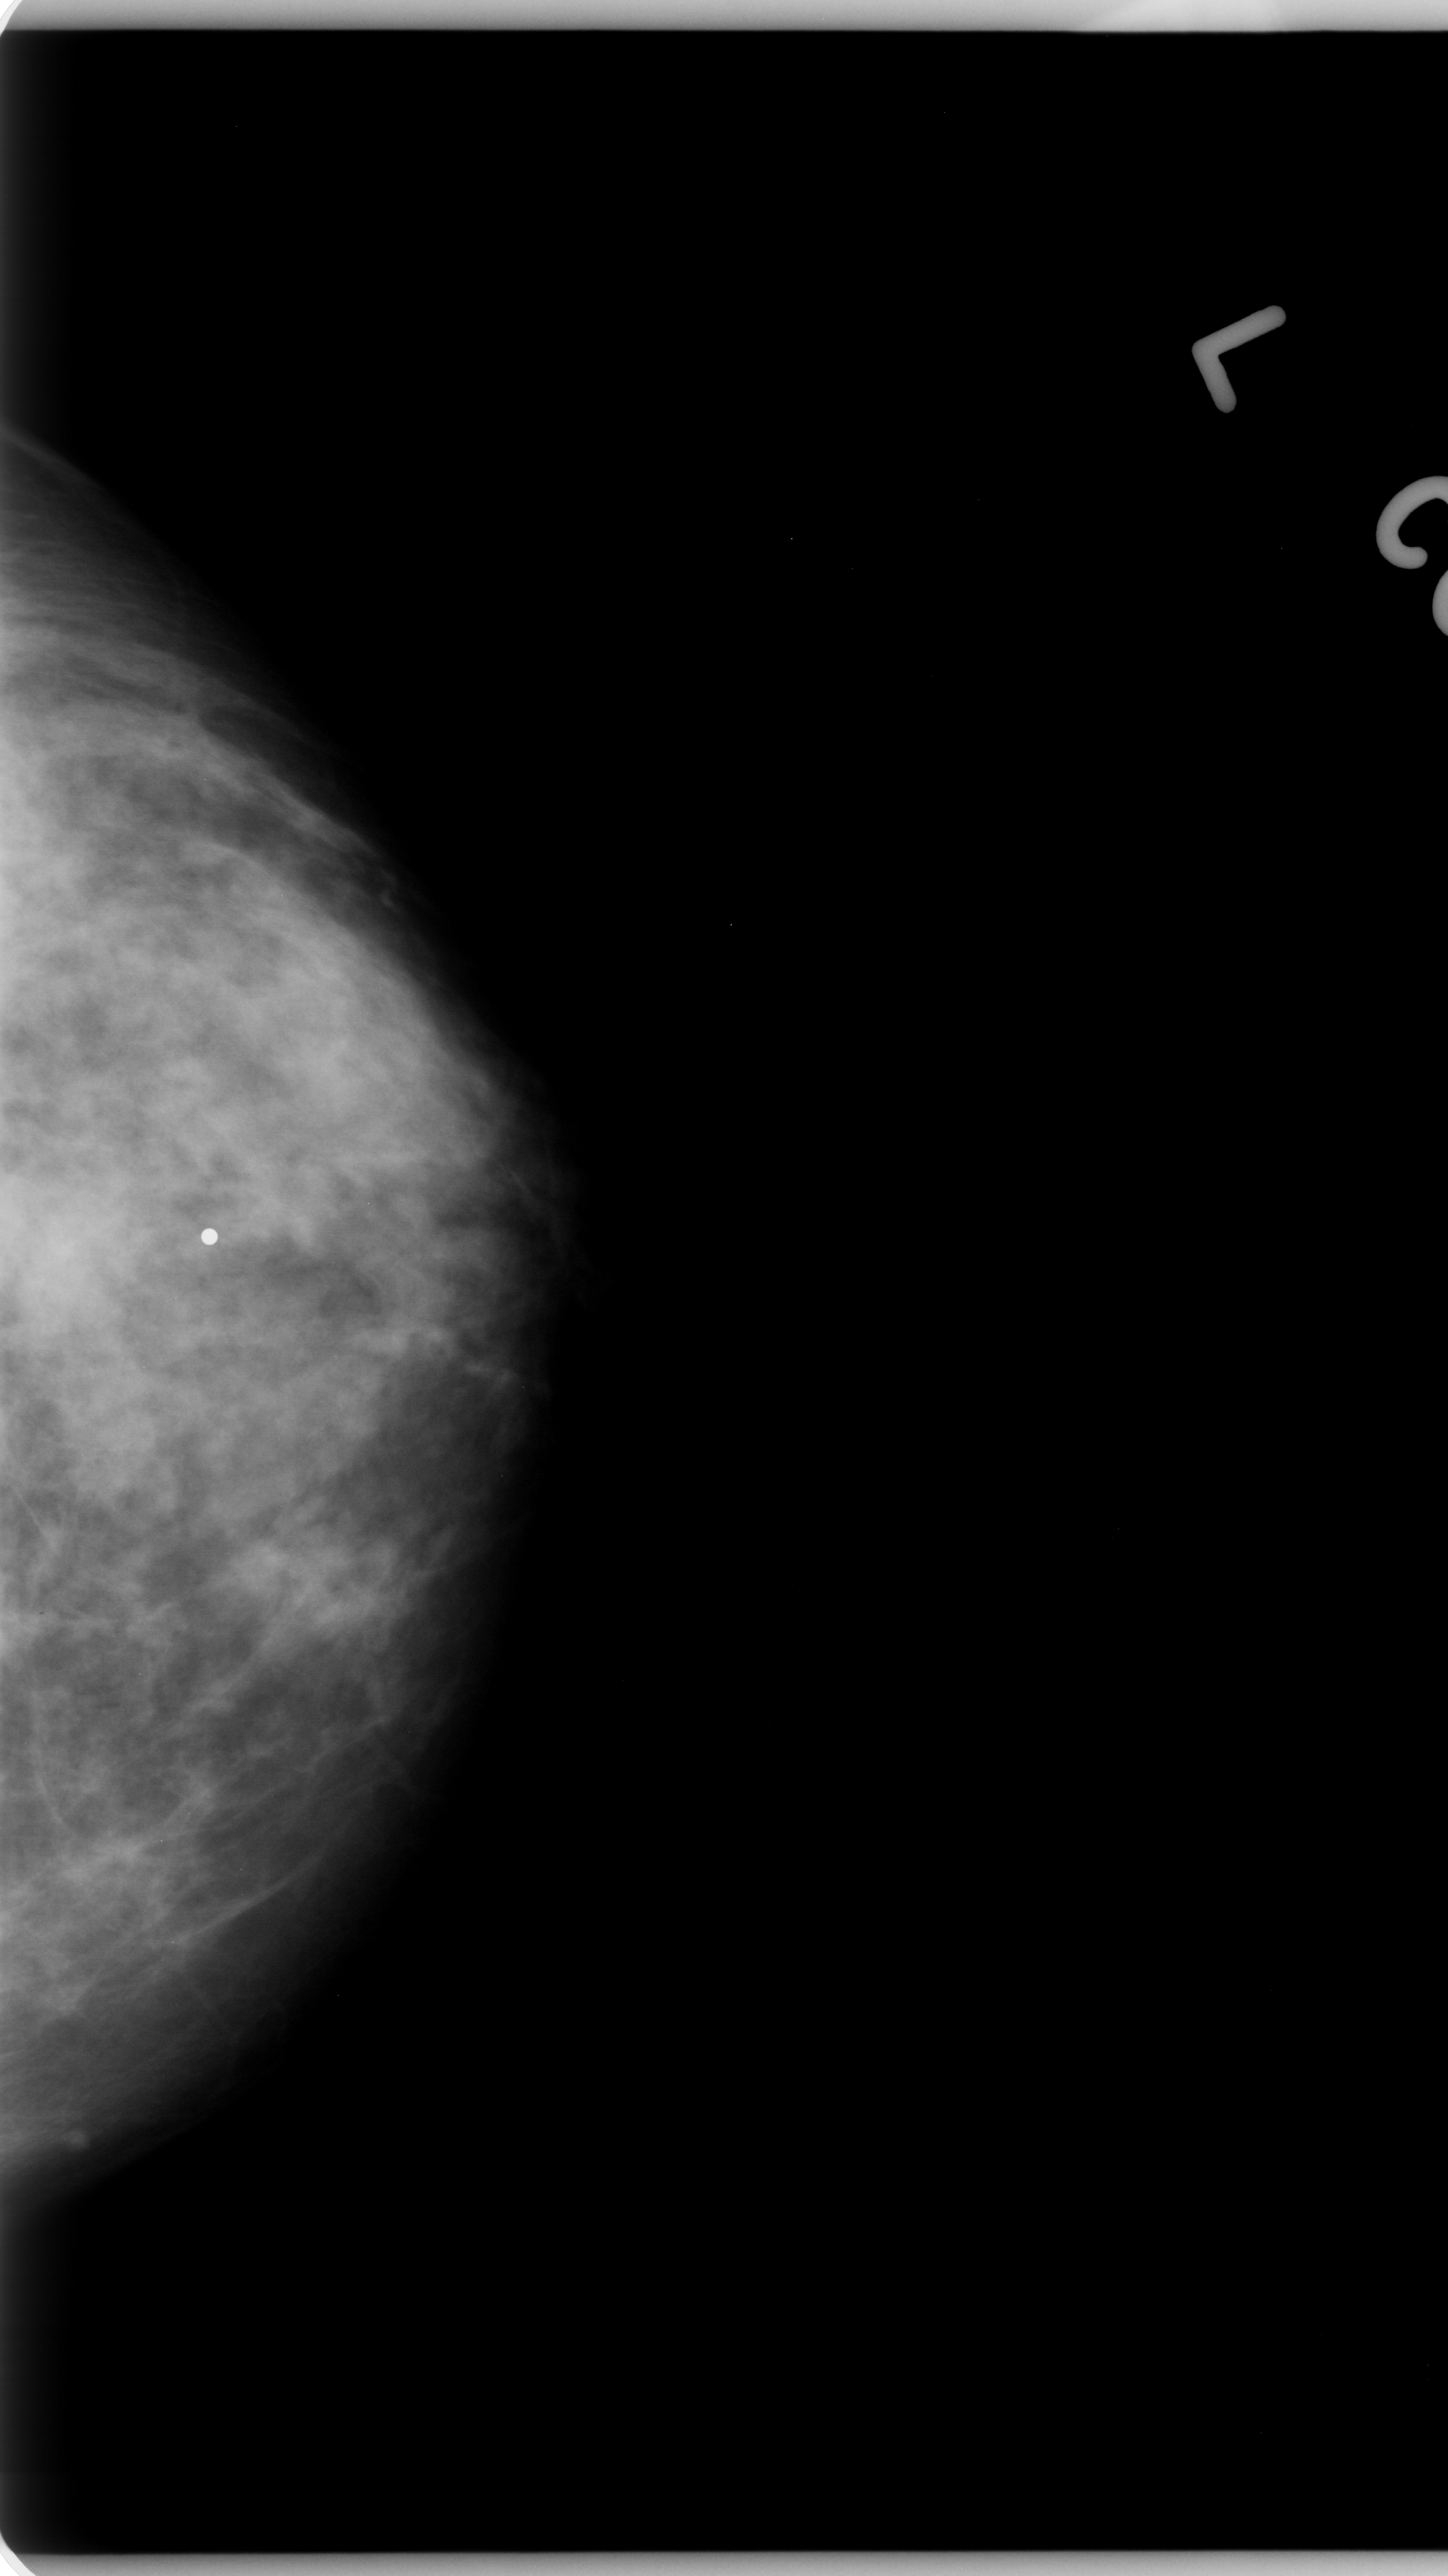
Mammogram (digitized film), left breast, craniocaudal (CC) view, BI-RADS breast density category 2 (scale 1–4).
- Abnormality record for this image: mass, shape lobulated, margins ill defined; BI-RADS assessment category 4; subtlety rating 1 on a 1 (subtle) to 5 (obvious) scale; pathology result (as recorded, not read from the image): malignant.